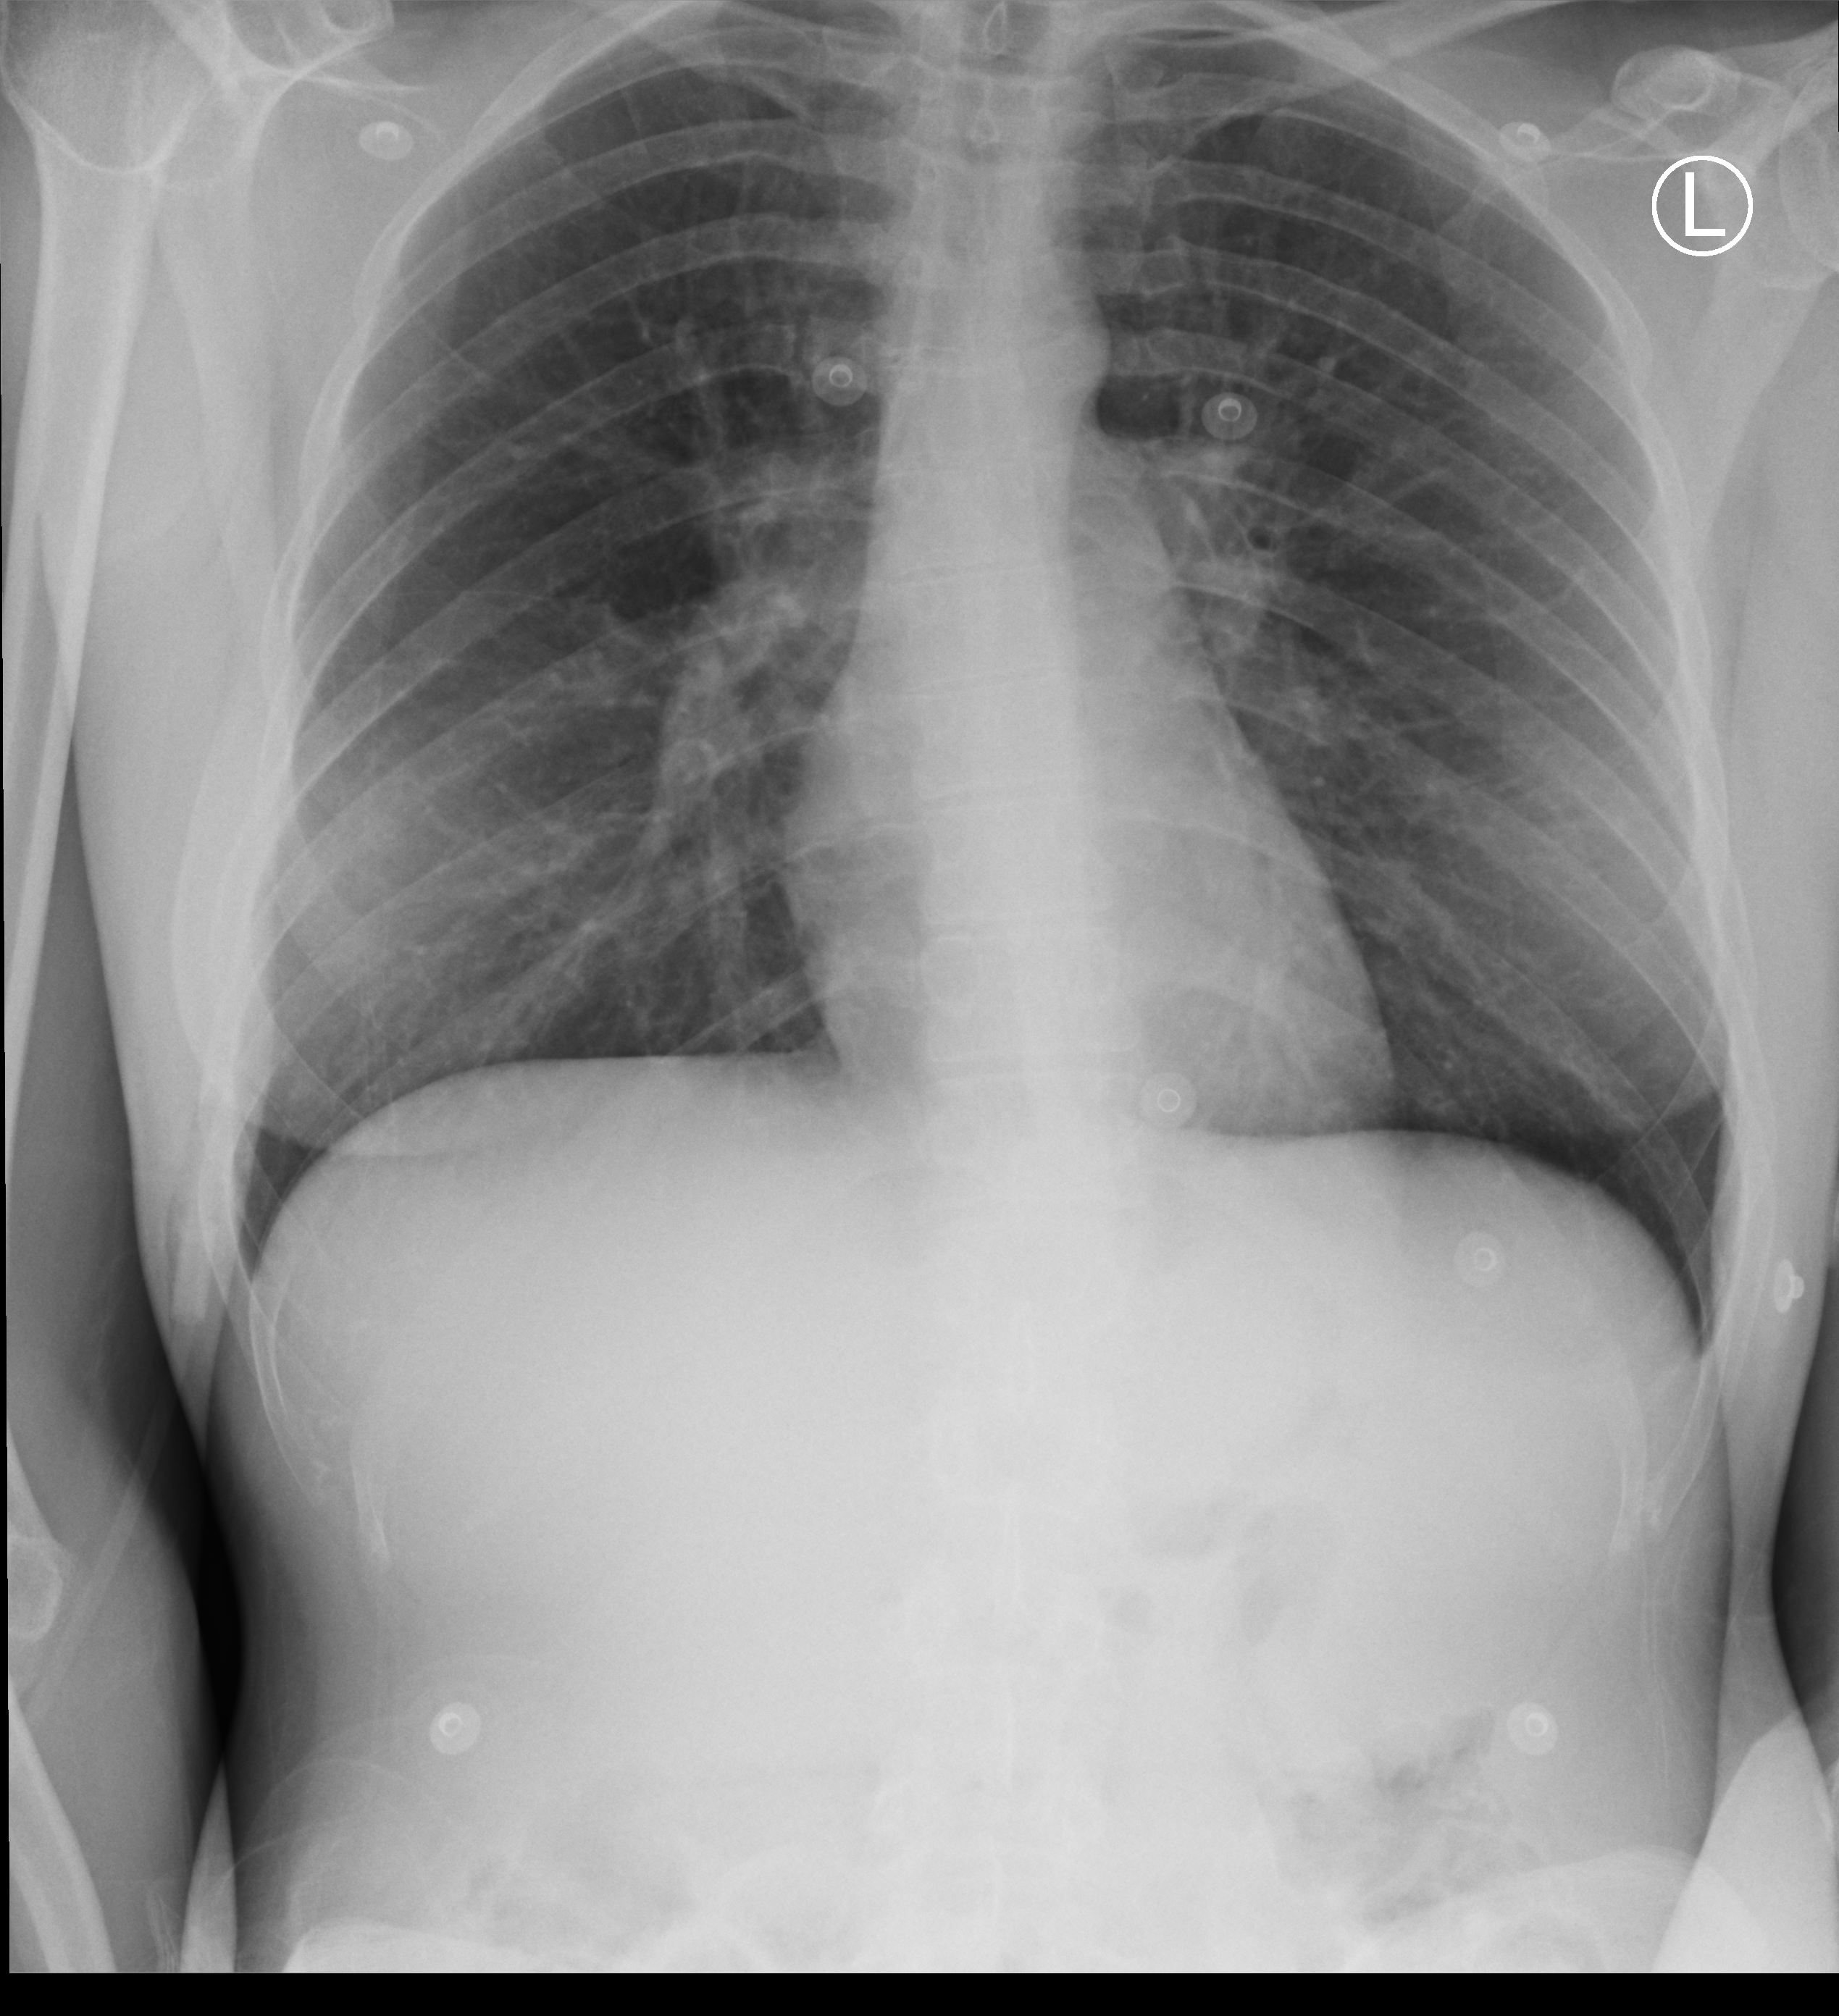
Chest X-ray (portable). Female patient hospitalised with COVID-19, age 18–59 years.
From the hospital-stay record, not from the radiograph (when in the stay this image was taken is not recorded):
- admitted to intensive care during this hospital stay: no
- length of hospital stay: 2 days
- mechanically ventilated during this hospital stay: no